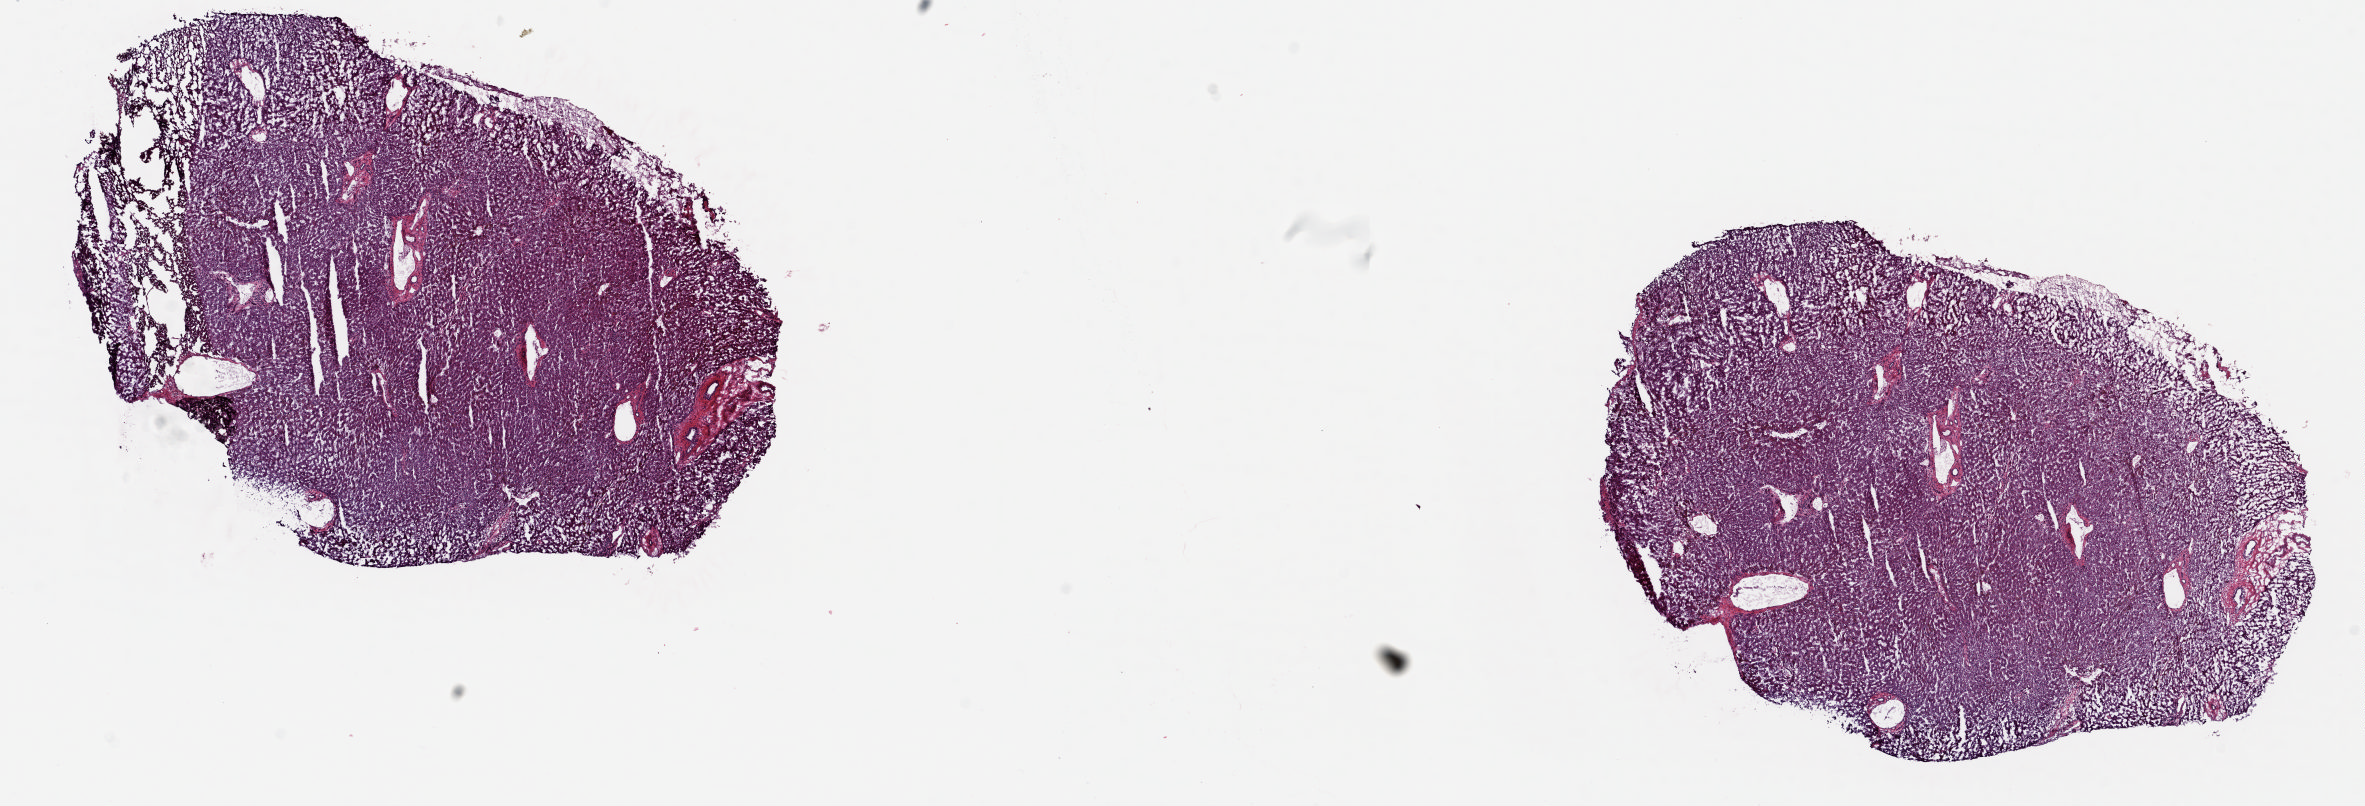
H&E-stained whole-slide image, low-resolution overview of the scanned area, about 18.8 x 6.4 mm (from a 20x scan). Frozen section from the top of the tissue portion. Liver, solid tissue normal (non-tumour tissue) sample. Male, age 81 years at initial diagnosis. Pathologist review of this section (percent, as recorded): tumour cells 0%, tumour nuclei 0%, normal cells 100%, stromal cells 0%, necrosis 0%. Infiltration values recorded for this section: lymphocyte infiltration 0%, monocyte infiltration 0%, neutrophil infiltration 0%.
* this section: solid tissue normal sample (biorepository sample class)
* patient diagnosis: Hepatocellular carcinoma, NOS